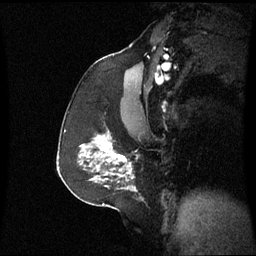
Breast MRI (dynamic contrast-enhanced), one sagittal slice. Slice 37 of 60 in the series (ordered by position). Dynamic contrast-enhanced series, image 2 of 3 at this slice position (ordered by acquisition). 1.5 T. TE 4.2 ms, TR 8.9 ms. 2.4 mm slice thickness. 256 × 256 image matrix, field of view 230 × 230 mm. Patient: female, 59 years. From the clinical record (not read from this slice): setting: breast cancer imaged before/during neoadjuvant chemotherapy; receptor status: triple-negative.
Annotated regions visible in this slice (semi-automatically segmented with operator editing):
- analysis volume of interest (the breast-tissue region the enhancement analysis was run in; not a lesion): bounding box [x1, y1, x2, y2] px = [86, 134, 138, 183]
- tumour enhancement mask (voxels above the 70 % enhancement threshold inside the analysis volume of interest): [97, 142, 130, 173]